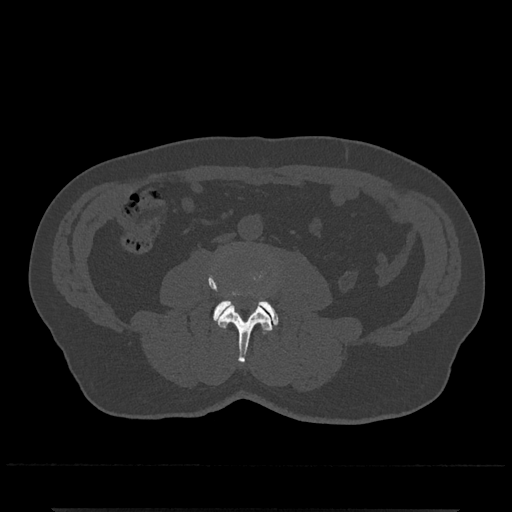
CT including the spine, one axial slice. Position 199 of 797 along the scan axis. Reconstruction kernel Br40s/3. 120 kVp. Bone window (W 1800 / L 400 HU). 0.5 mm slice thickness. 512 × 512 image matrix. Male patient, age 67 years. Case-level facts recorded for this patient, not image findings: primary cancer: prostate.
Structures marked on this image (semi-automatic segmentation, software-assisted and operator-edited):
- L3 vertebra: bounding box <208,272,273,363> (left, top, right, bottom; pixels)
- L4 vertebra: <214,299,278,326>